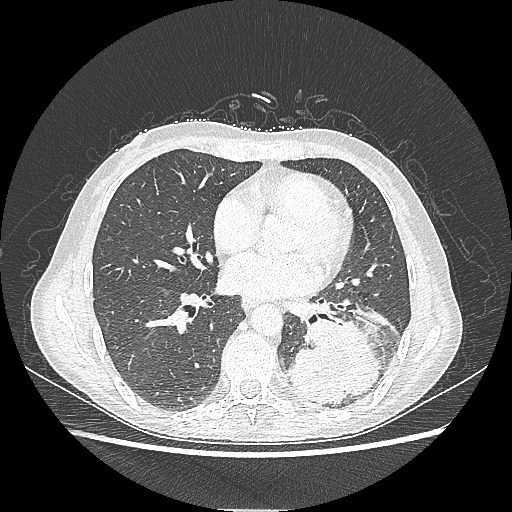
Chest CT, one axial slice; slice 100 of 220 in the series (ordered by position); lung window (W 1500 / L -600 HU); 1.25 mm slice thickness; 512 × 512 image matrix. Patient: female, 53 years. From the clinical record (not read from this slice): clinical TNM (as recorded): T3 N0 M0.
Outlined on this slice (rectangle marked by the reading radiologist):
- lung tumour (recorded histology: adenocarcinoma): bounding box (x1, y1, x2, y2) in pixels: (283, 314, 381, 407)